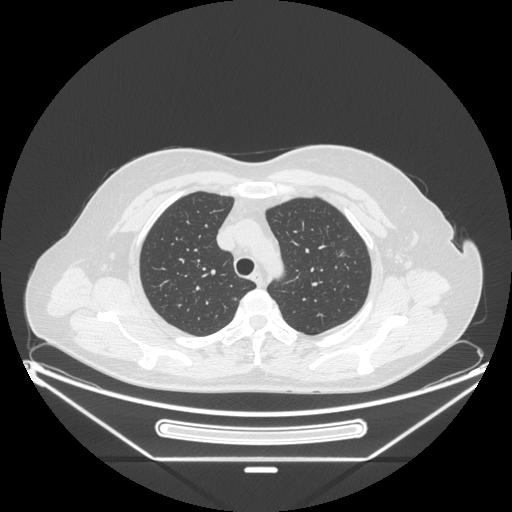
Chest CT, one axial slice; position 170 of 226 along the scan axis; reconstruction kernel STANDARD; 120 kVp; lung window (W 1500 / L -600 HU); 1.25 mm slice thickness; 512 × 512 image matrix, field of view 447 × 447 mm. Patient: female, 54 years. From the clinical record (not read from this slice): clinical TNM (as recorded): T1c N0 M0; histopathological grade: G1.
Annotated regions visible in this slice (rectangle marked by the reading radiologist):
- lung tumour (recorded histology: adenocarcinoma): bounding box <330,244,354,271> (left, top, right, bottom; pixels)